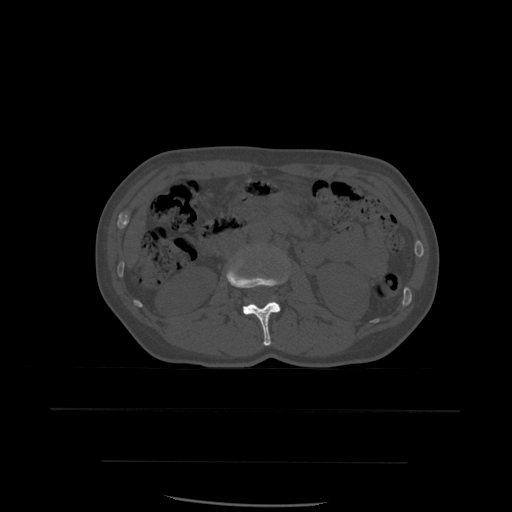
CT including the spine, one axial slice; slice 218 of 574 in the series (ordered by position); bone window (W 1800 / L 400 HU); 1.25 mm slice thickness; 512 × 512 image matrix. Patient age 48 years. Case-level facts recorded for this patient, not image findings: primary cancer: lung.
Outlined on this slice (semi-automatic segmentation, software-assisted and operator-edited):
- L2 vertebra: bounding box <227,253,289,346> (left, top, right, bottom; pixels)